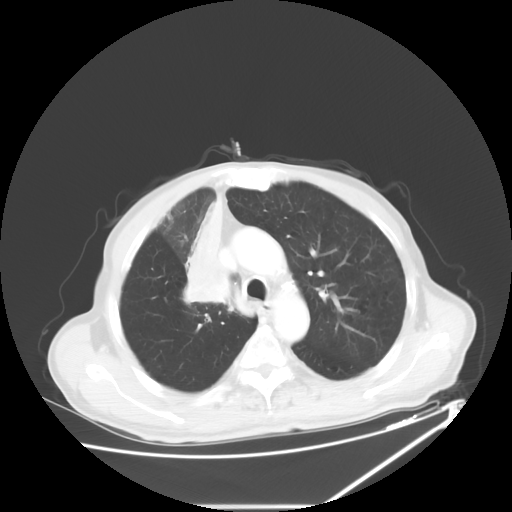
Chest CT, one axial slice. Position 44 of 60 along the scan axis. Reconstruction kernel STANDARD. 120 kVp. Lung window (W 1500 / L -600 HU). 512 × 512 image matrix, field of view 410 × 410 mm. Male patient, age 73 years. From the clinical record (not read from this slice): clinical TNM (as recorded): T2a N1 M0.
Outlined on this slice (bounding box drawn by a radiologist):
- lung tumour (recorded histology: squamous cell carcinoma): bounding box <181,194,234,310> (left, top, right, bottom; pixels)